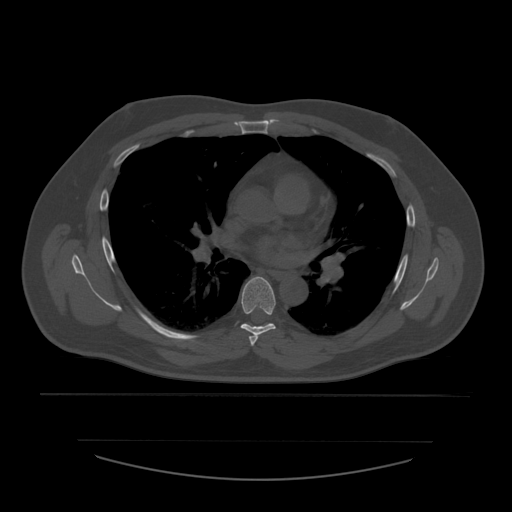
CT including the spine, one axial slice; slice 378 of 532 in the series (ordered by position); reconstruction kernel STANDARD; 120 kVp; bone window (W 1800 / L 400 HU); 1.25 mm slice thickness; 512 × 512 image matrix, field of view 441 × 441 mm. Patient age 44 years. Case-level facts recorded for this patient, not image findings: primary cancer: soft tissue sarcoma.
Structures marked on this image (semi-automatic segmentation, software-assisted and operator-edited):
- T5 vertebra: bounding box <249,335,259,346> (left, top, right, bottom; pixels)
- T6 vertebra: <241,277,276,336>